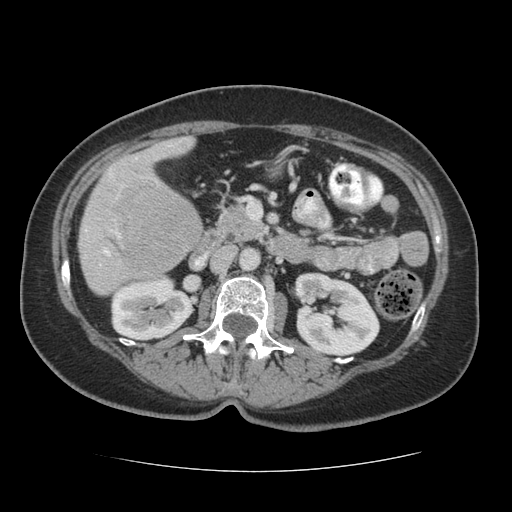
Contrast-enhanced abdominal CT (liver protocol), one axial slice. Slice 18 of 75 in the series (ordered by position). Reconstruction kernel STANDARD. Soft-tissue window (W 400 / L 40 HU). 2.5 mm slice thickness. 512 × 512 image matrix, field of view 360 × 360 mm. From the clinical record (not read from this slice): diagnosis: hepatocellular carcinoma (patient treated with transarterial chemoembolisation; whether this scan precedes or follows treatment is not stated here); TNM stage (as recorded): Stage-I; Child-Pugh class: A; tumour nodularity: uninodular.
Structures marked on this image (semi-automatic segmentation, software-assisted and operator-edited):
- liver parenchyma outside the tumour (the mass and vessels are separate outlines, so this box may not span the whole liver): bounding box (x1, y1, x2, y2) in pixels: (78, 136, 202, 294)
- mass: (104, 167, 202, 276)
- liver vessels: (85, 144, 173, 266)